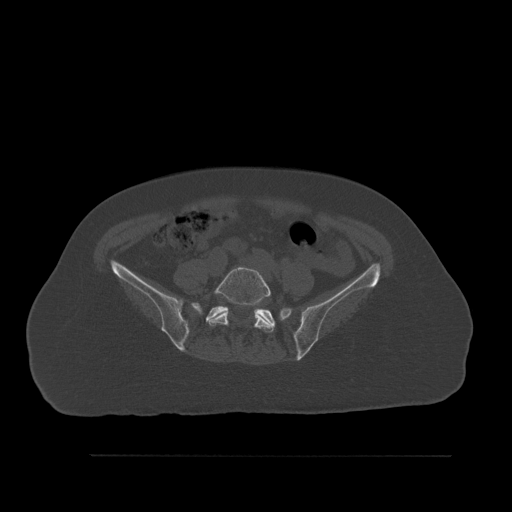
CT including the spine, one axial slice; position 184 of 527 along the scan axis; bone window (W 1800 / L 400 HU); 1.5 mm slice thickness; 512 × 512 image matrix, field of view 470 × 470 mm. Female patient, age 73 years. Case-level facts recorded for this patient, not image findings: primary cancer: breast; vertebrae with lytic lesions (as recorded): L2.
Outlined on this slice (semi-automatically segmented with operator editing):
- L5 vertebra: bounding box [x1, y1, x2, y2] px = [206, 266, 274, 337]